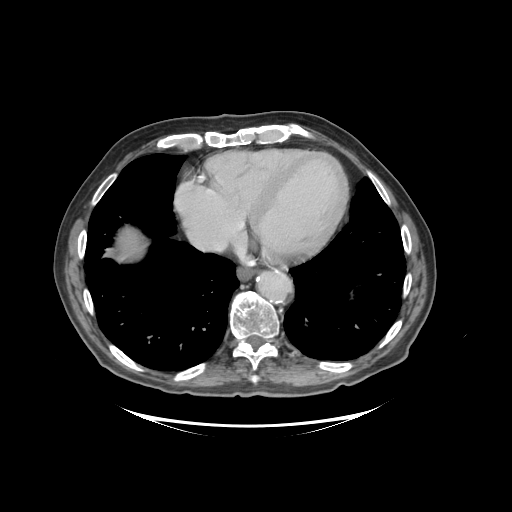
Contrast-enhanced abdominal CT (liver protocol), one axial slice; position 92 of 99 along the scan axis; reconstruction kernel STANDARD; 140 kVp; soft-tissue window (W 400 / L 40 HU); 2.5 mm slice thickness; 512 × 512 image matrix. Case-level facts recorded for this patient, not image findings: diagnosis: hepatocellular carcinoma (patient treated with transarterial chemoembolisation; whether this scan precedes or follows treatment is not stated here); TNM stage (as recorded): Stage-I; Child-Pugh class: A; tumour differentiation: moderately differentiated; tumour nodularity: uninodular.
Outlined on this slice (semi-automatic segmentation, software-assisted and operator-edited):
- liver parenchyma outside the tumour (the mass and vessels are separate outlines, so this box may not span the whole liver): box from (x=116, y=228) to (x=144, y=258) px